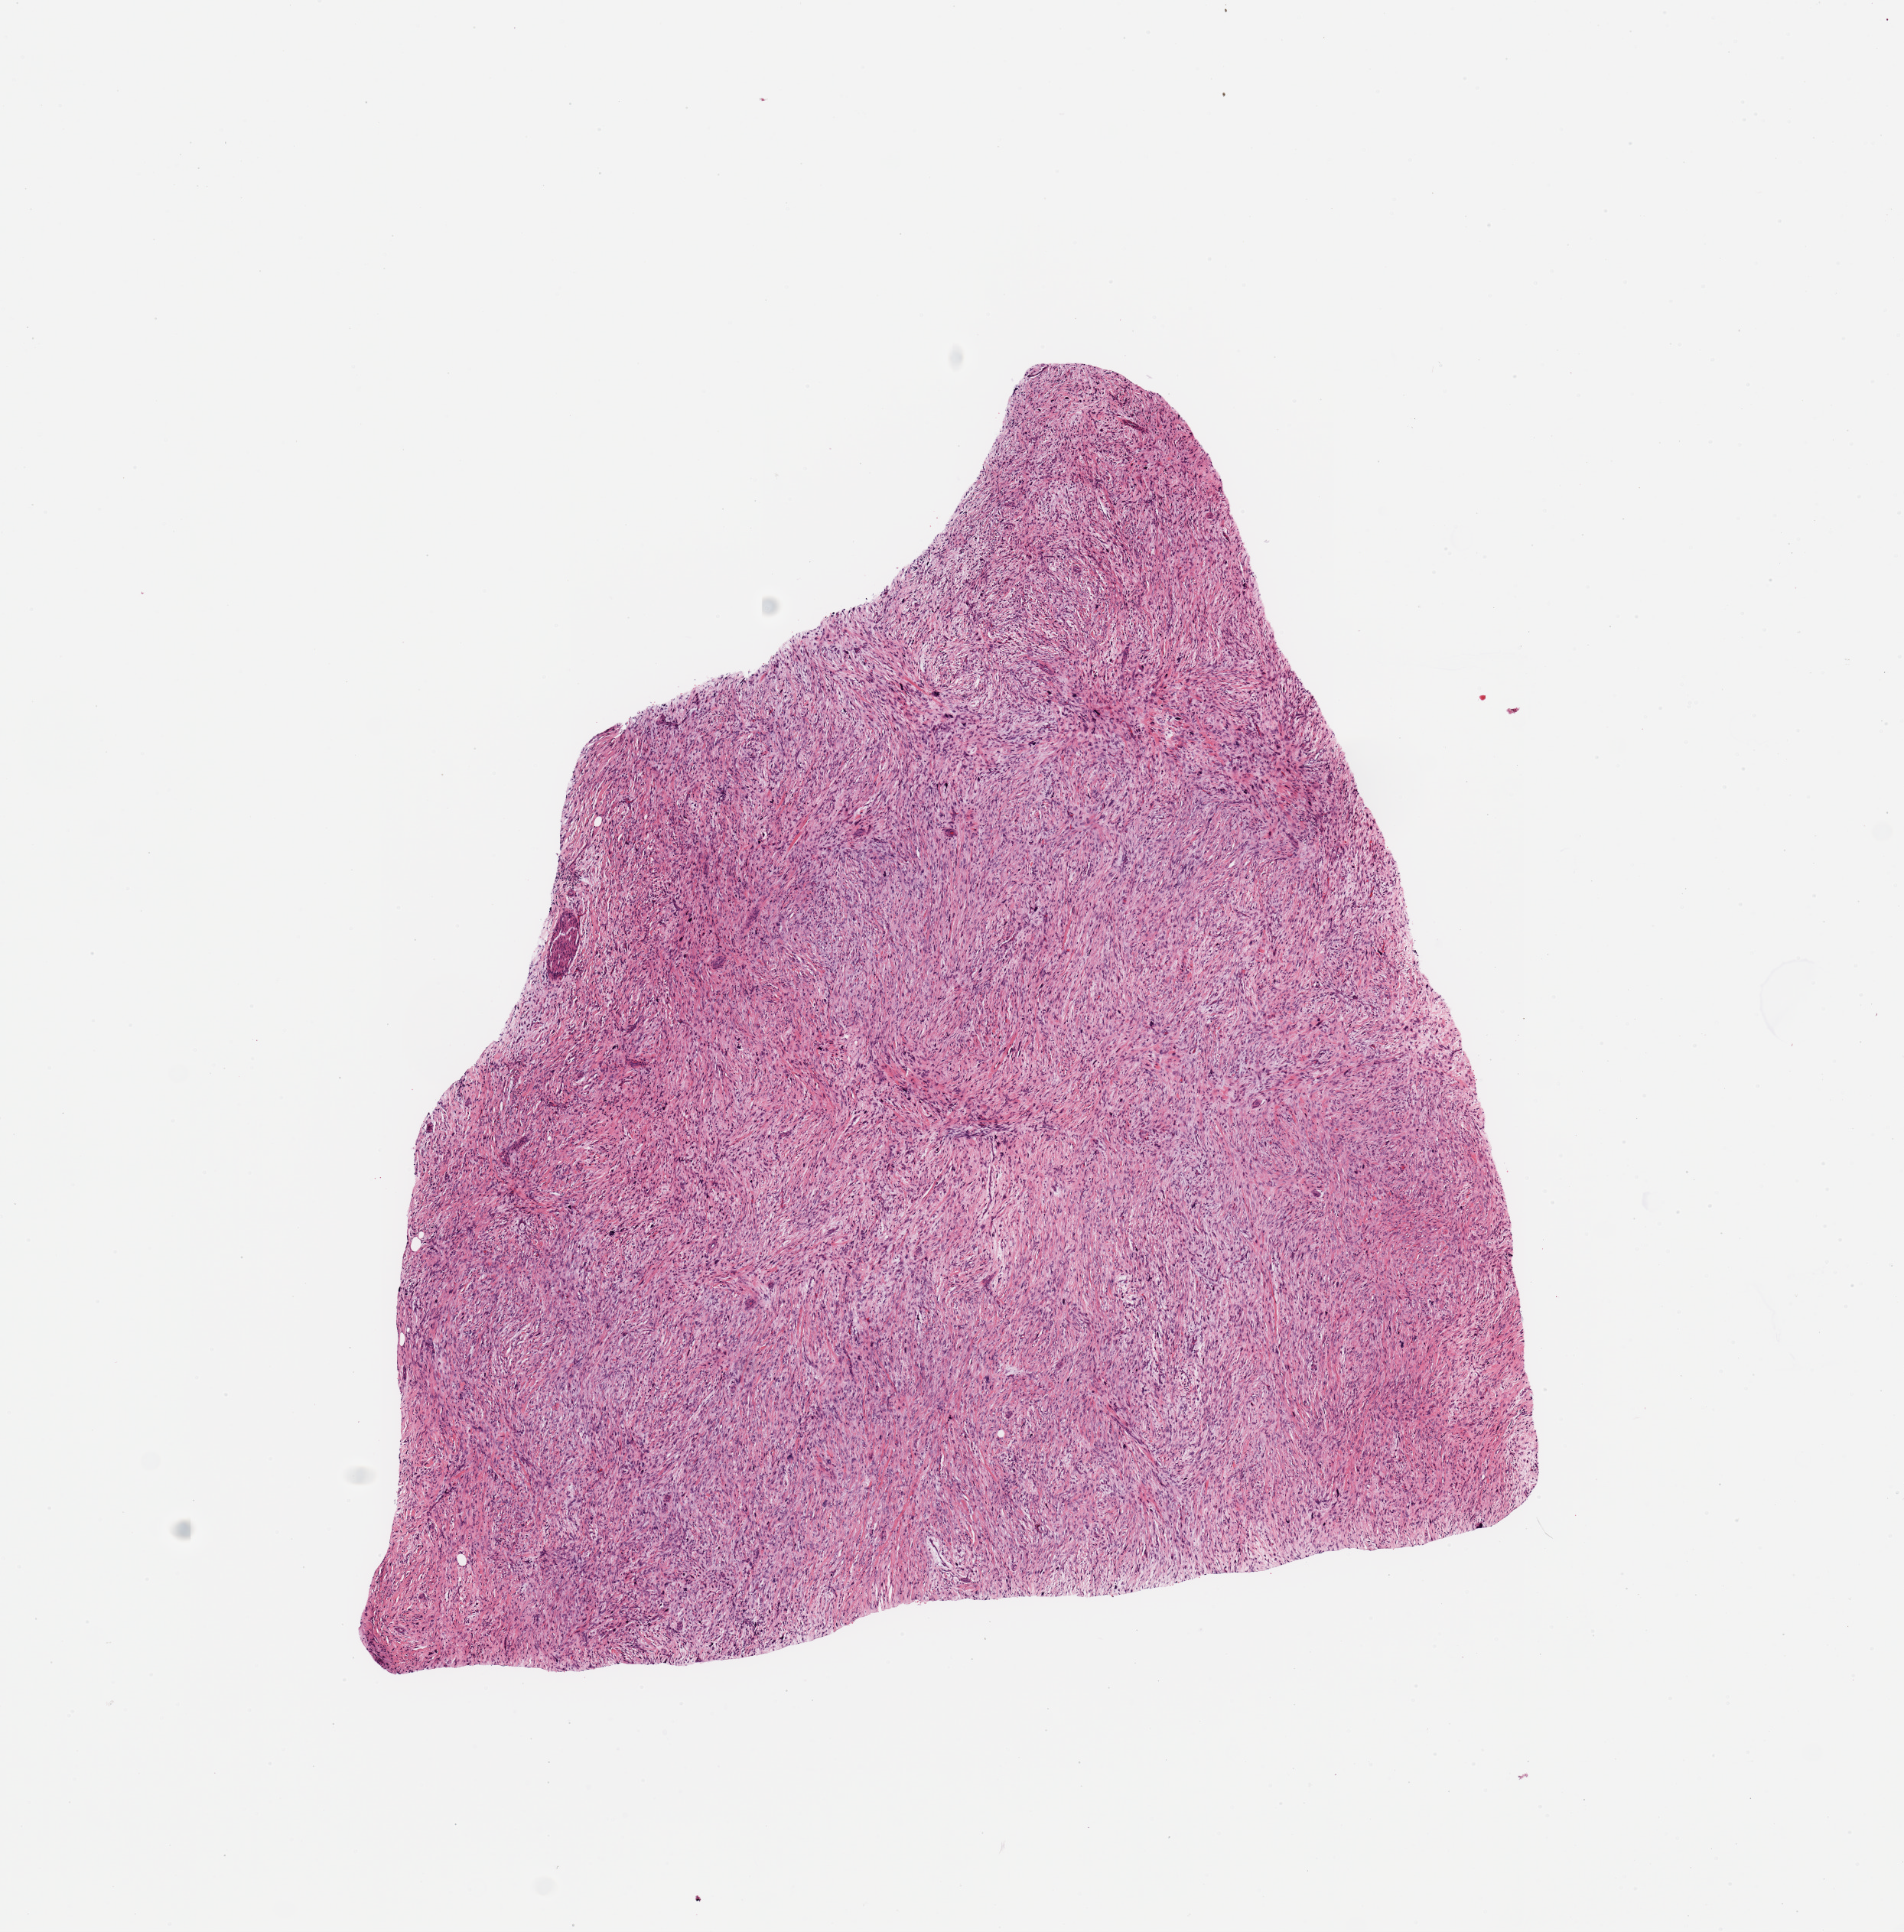
Hematoxylin and eosin (H&E) stained whole-slide image, shown as a low-resolution overview of the whole scanned area (about 9.8 x 10.0 mm, acquisition: 20x scan), tumour tissue sample. Patient: male, age 65 years.
Patient diagnosis (cohort enrolment): sarcoma (site not recorded at cohort level).